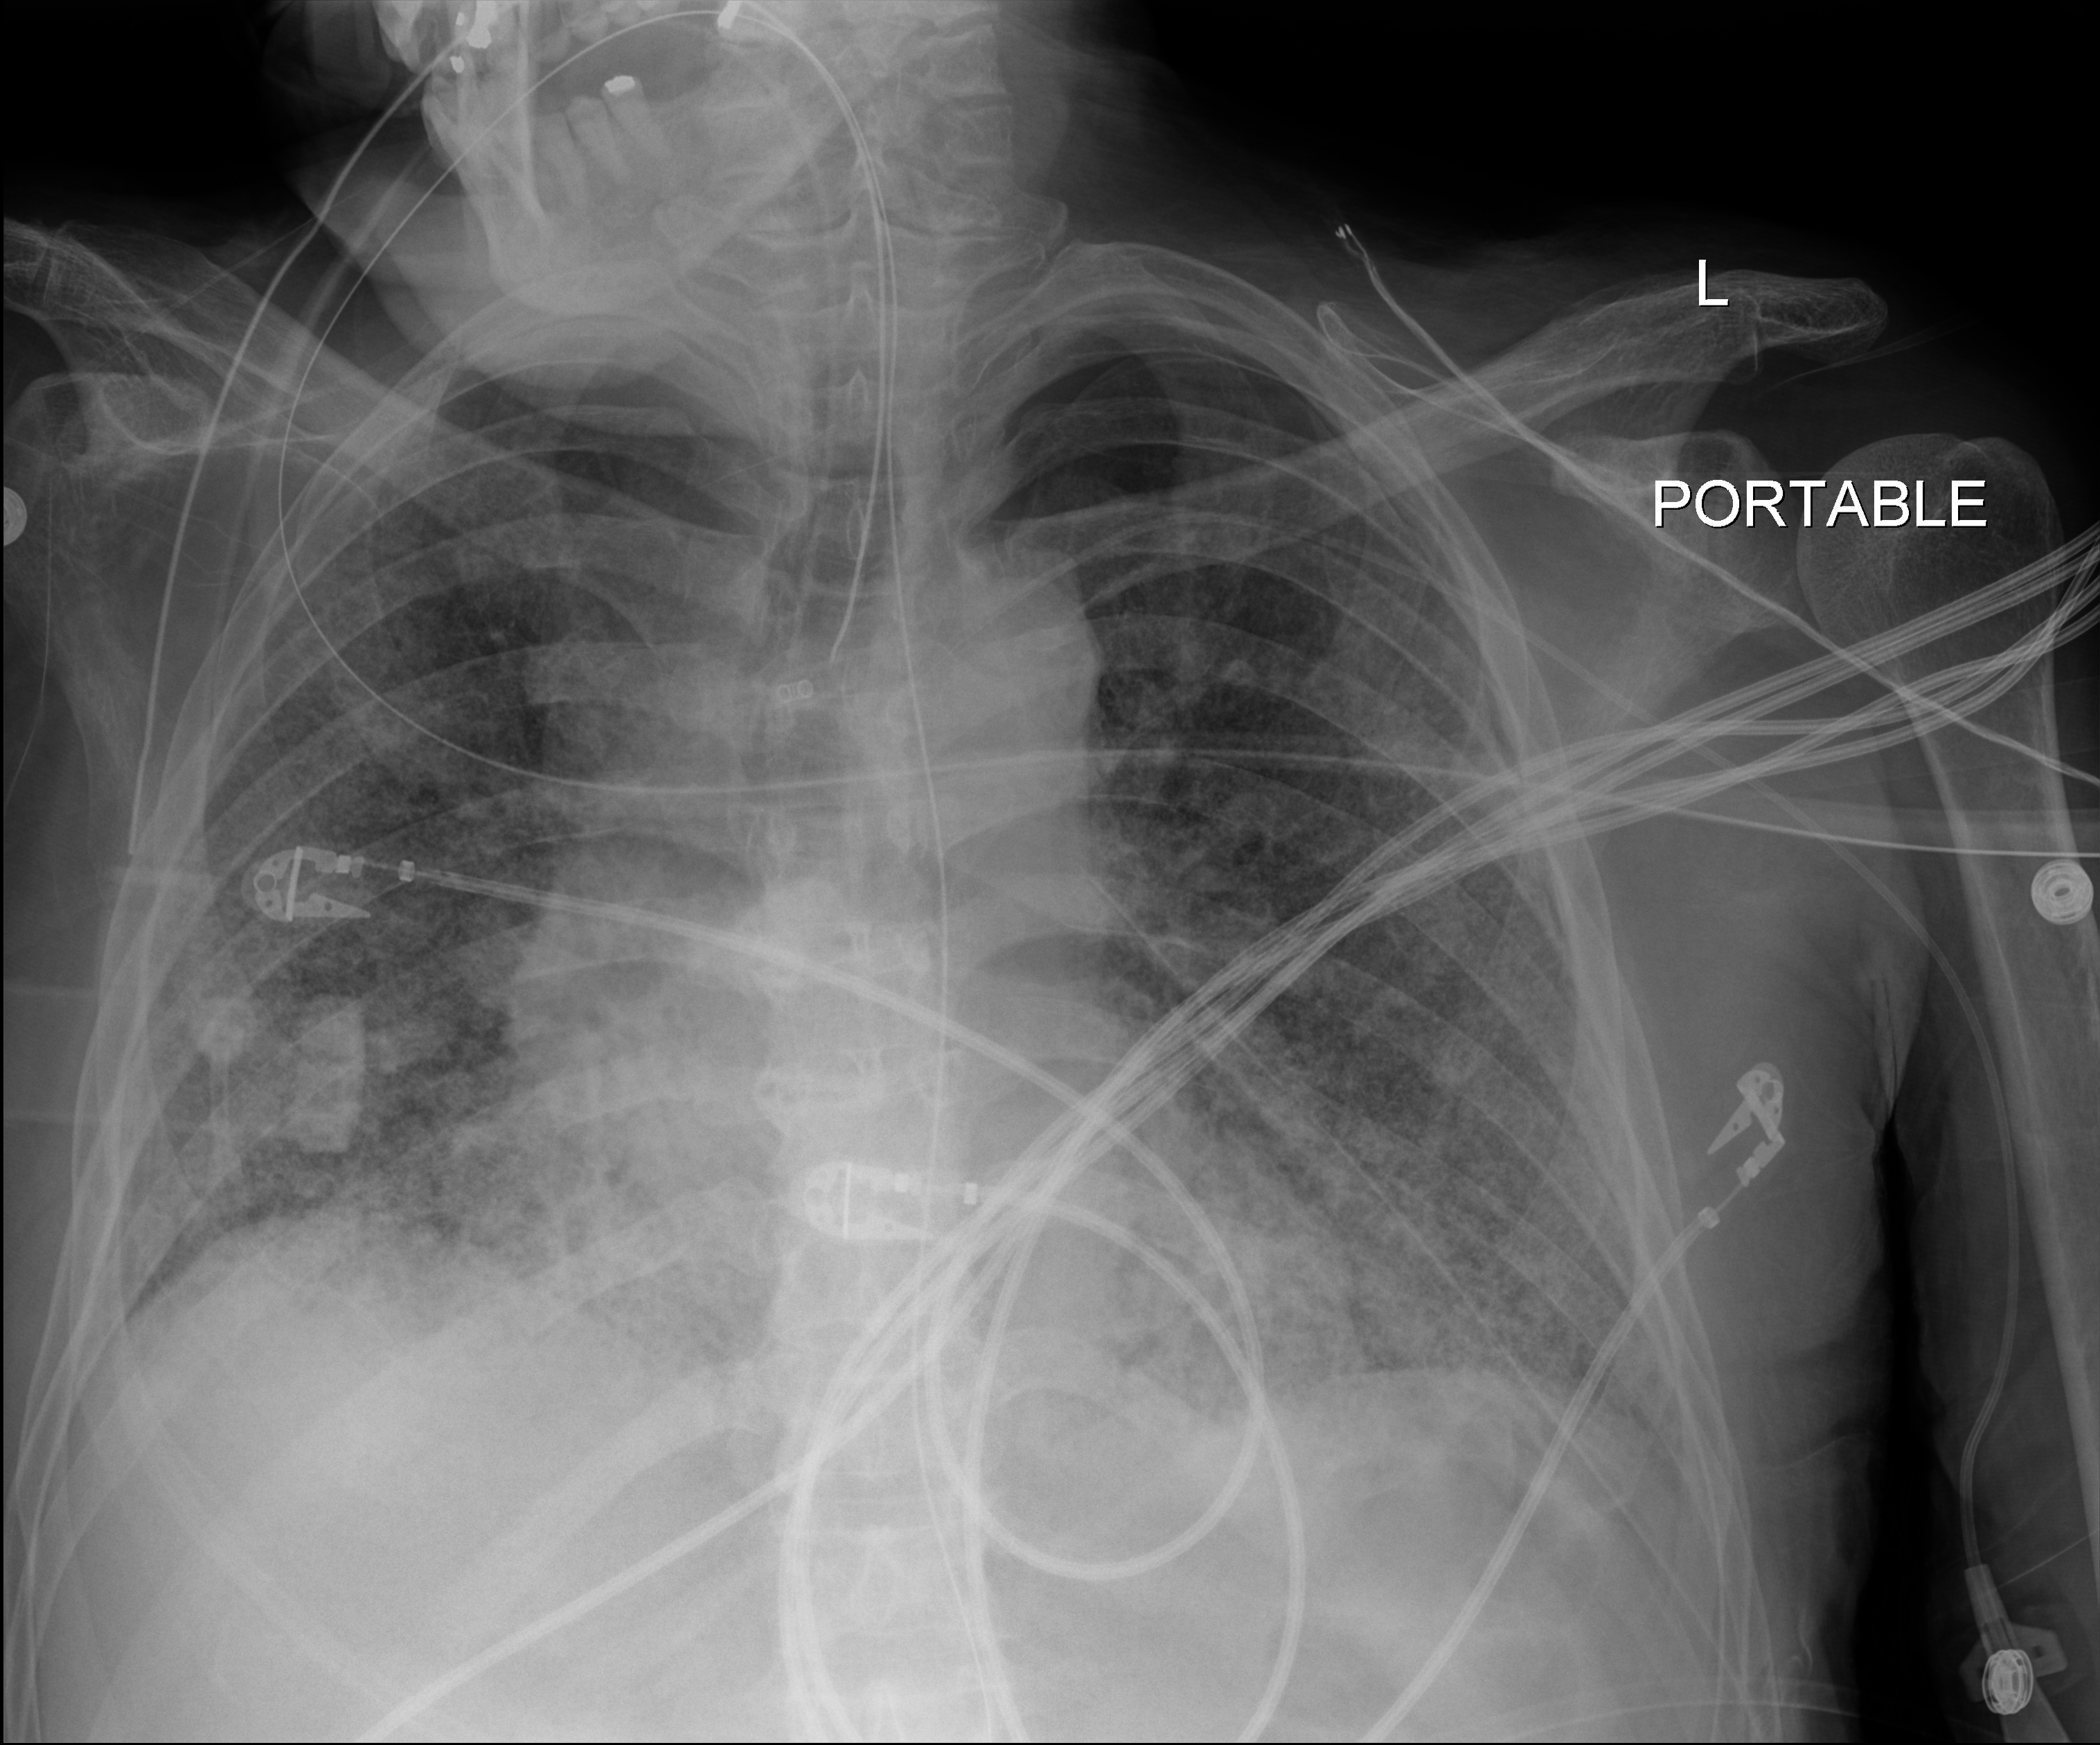
Bedside chest radiograph (digital radiography); anteroposterior (AP) projection. Patient hospitalised with COVID-19; male, aged 60–74 years.
From the hospital-stay record, not from the radiograph (when in the stay this image was taken is not recorded): mechanically ventilated during this hospital stay: yes.